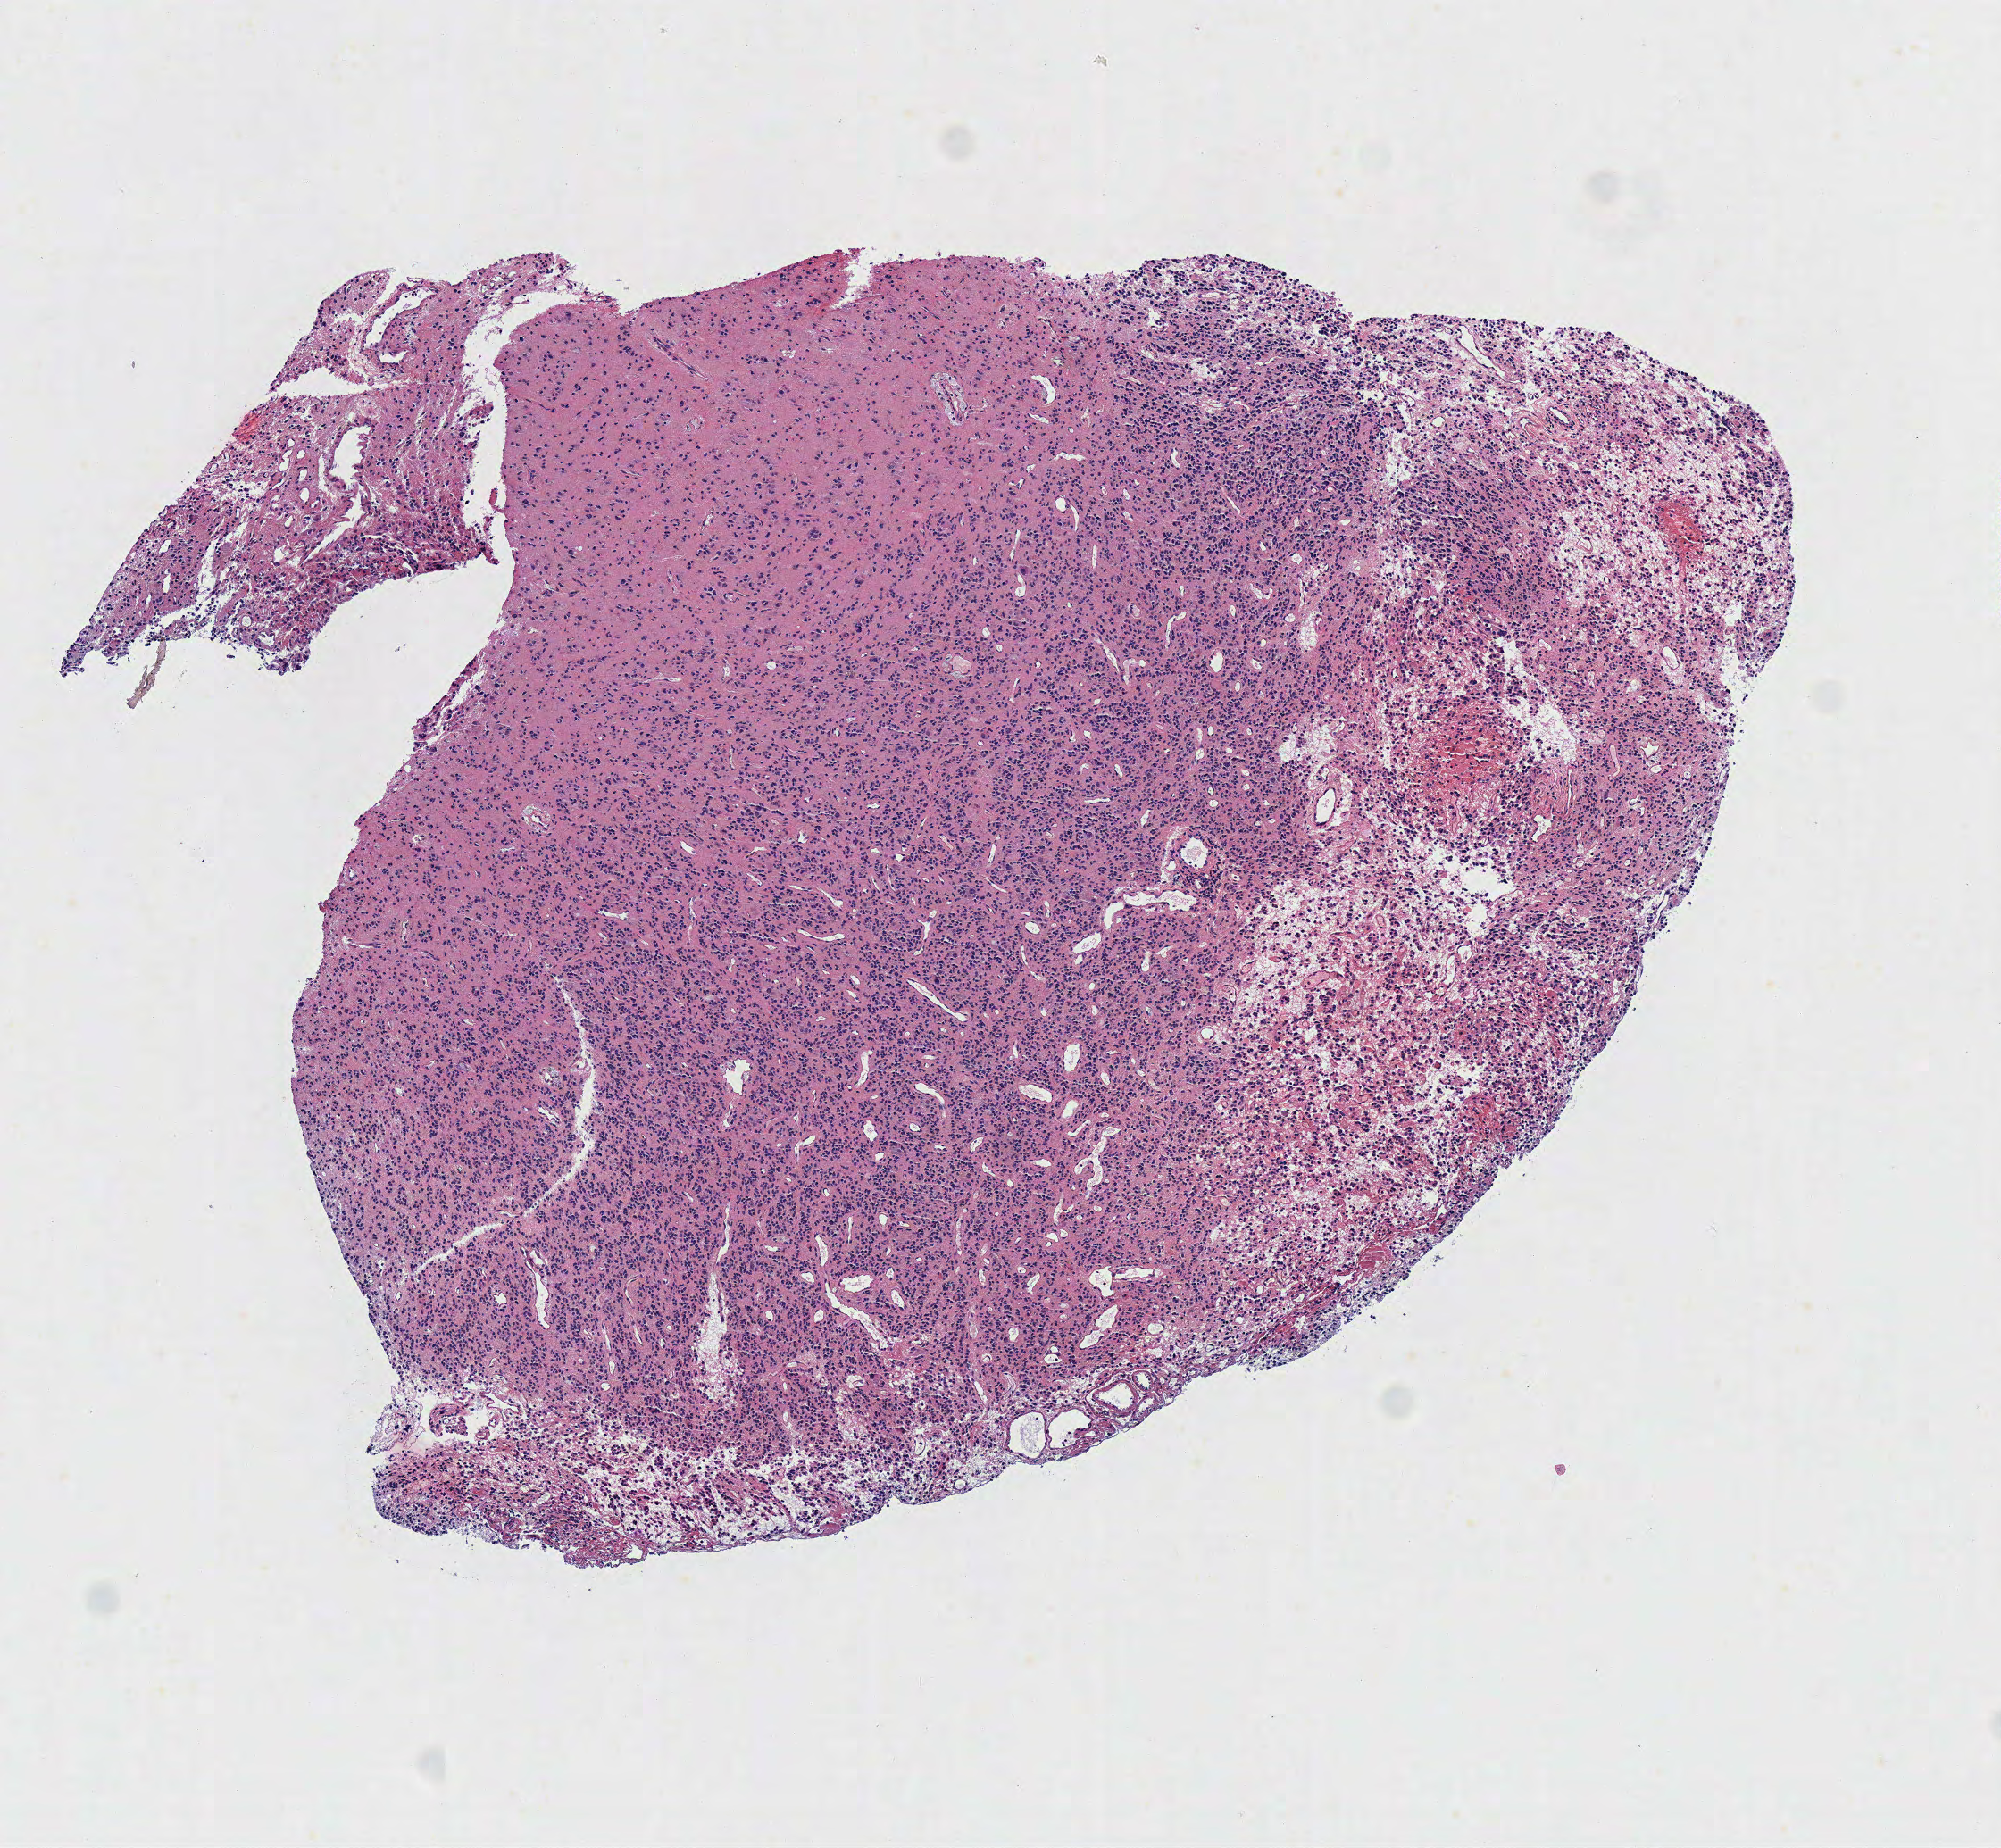
Hematoxylin and eosin (H&E) stained whole-slide image — a low-resolution overview of the entire scanned area, about 4.4 x 4.1 mm (slide scanned at 40x); frozen section; brain, primary tumour sample. Patient: male, age at initial diagnosis 45 years. Histologic grade: G3 (poorly differentiated). Composition of this section per pathologist review: tumour cells 100%, tumour nuclei 80%, normal cells 0%, stromal cells 0%, necrosis 0%.
Pathologic diagnosis: Oligodendroglioma, anaplastic (cerebrum).